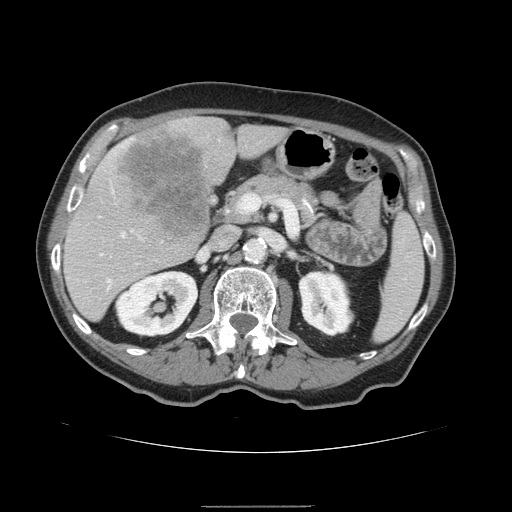
Contrast-enhanced abdominal CT, one axial slice. Slice 77 of 168 in the series (ordered by position). 120 kVp. Intravenous contrast given. Soft-tissue window (W 400 / L 40 HU). 512 × 512 image matrix, field of view 386 × 386 mm. Male patient, age 74 years. From the clinical record (not read from this slice): diagnosis: colorectal cancer liver metastases, imaged before liver resection; multiple liver metastases: no; largest metastasis: 14.5 cm.
Structures marked on this image (outlined manually by an expert reader):
- hepatic veins: bounding box (x1, y1, x2, y2) in pixels: (109, 232, 125, 281)
- liver: (63, 117, 288, 322)
- planned liver remnant (the part of the liver to remain after resection): (64, 125, 287, 322)
- portal vein (with intrahepatic branches): (99, 253, 158, 262)
- liver metastasis: (117, 125, 214, 242)